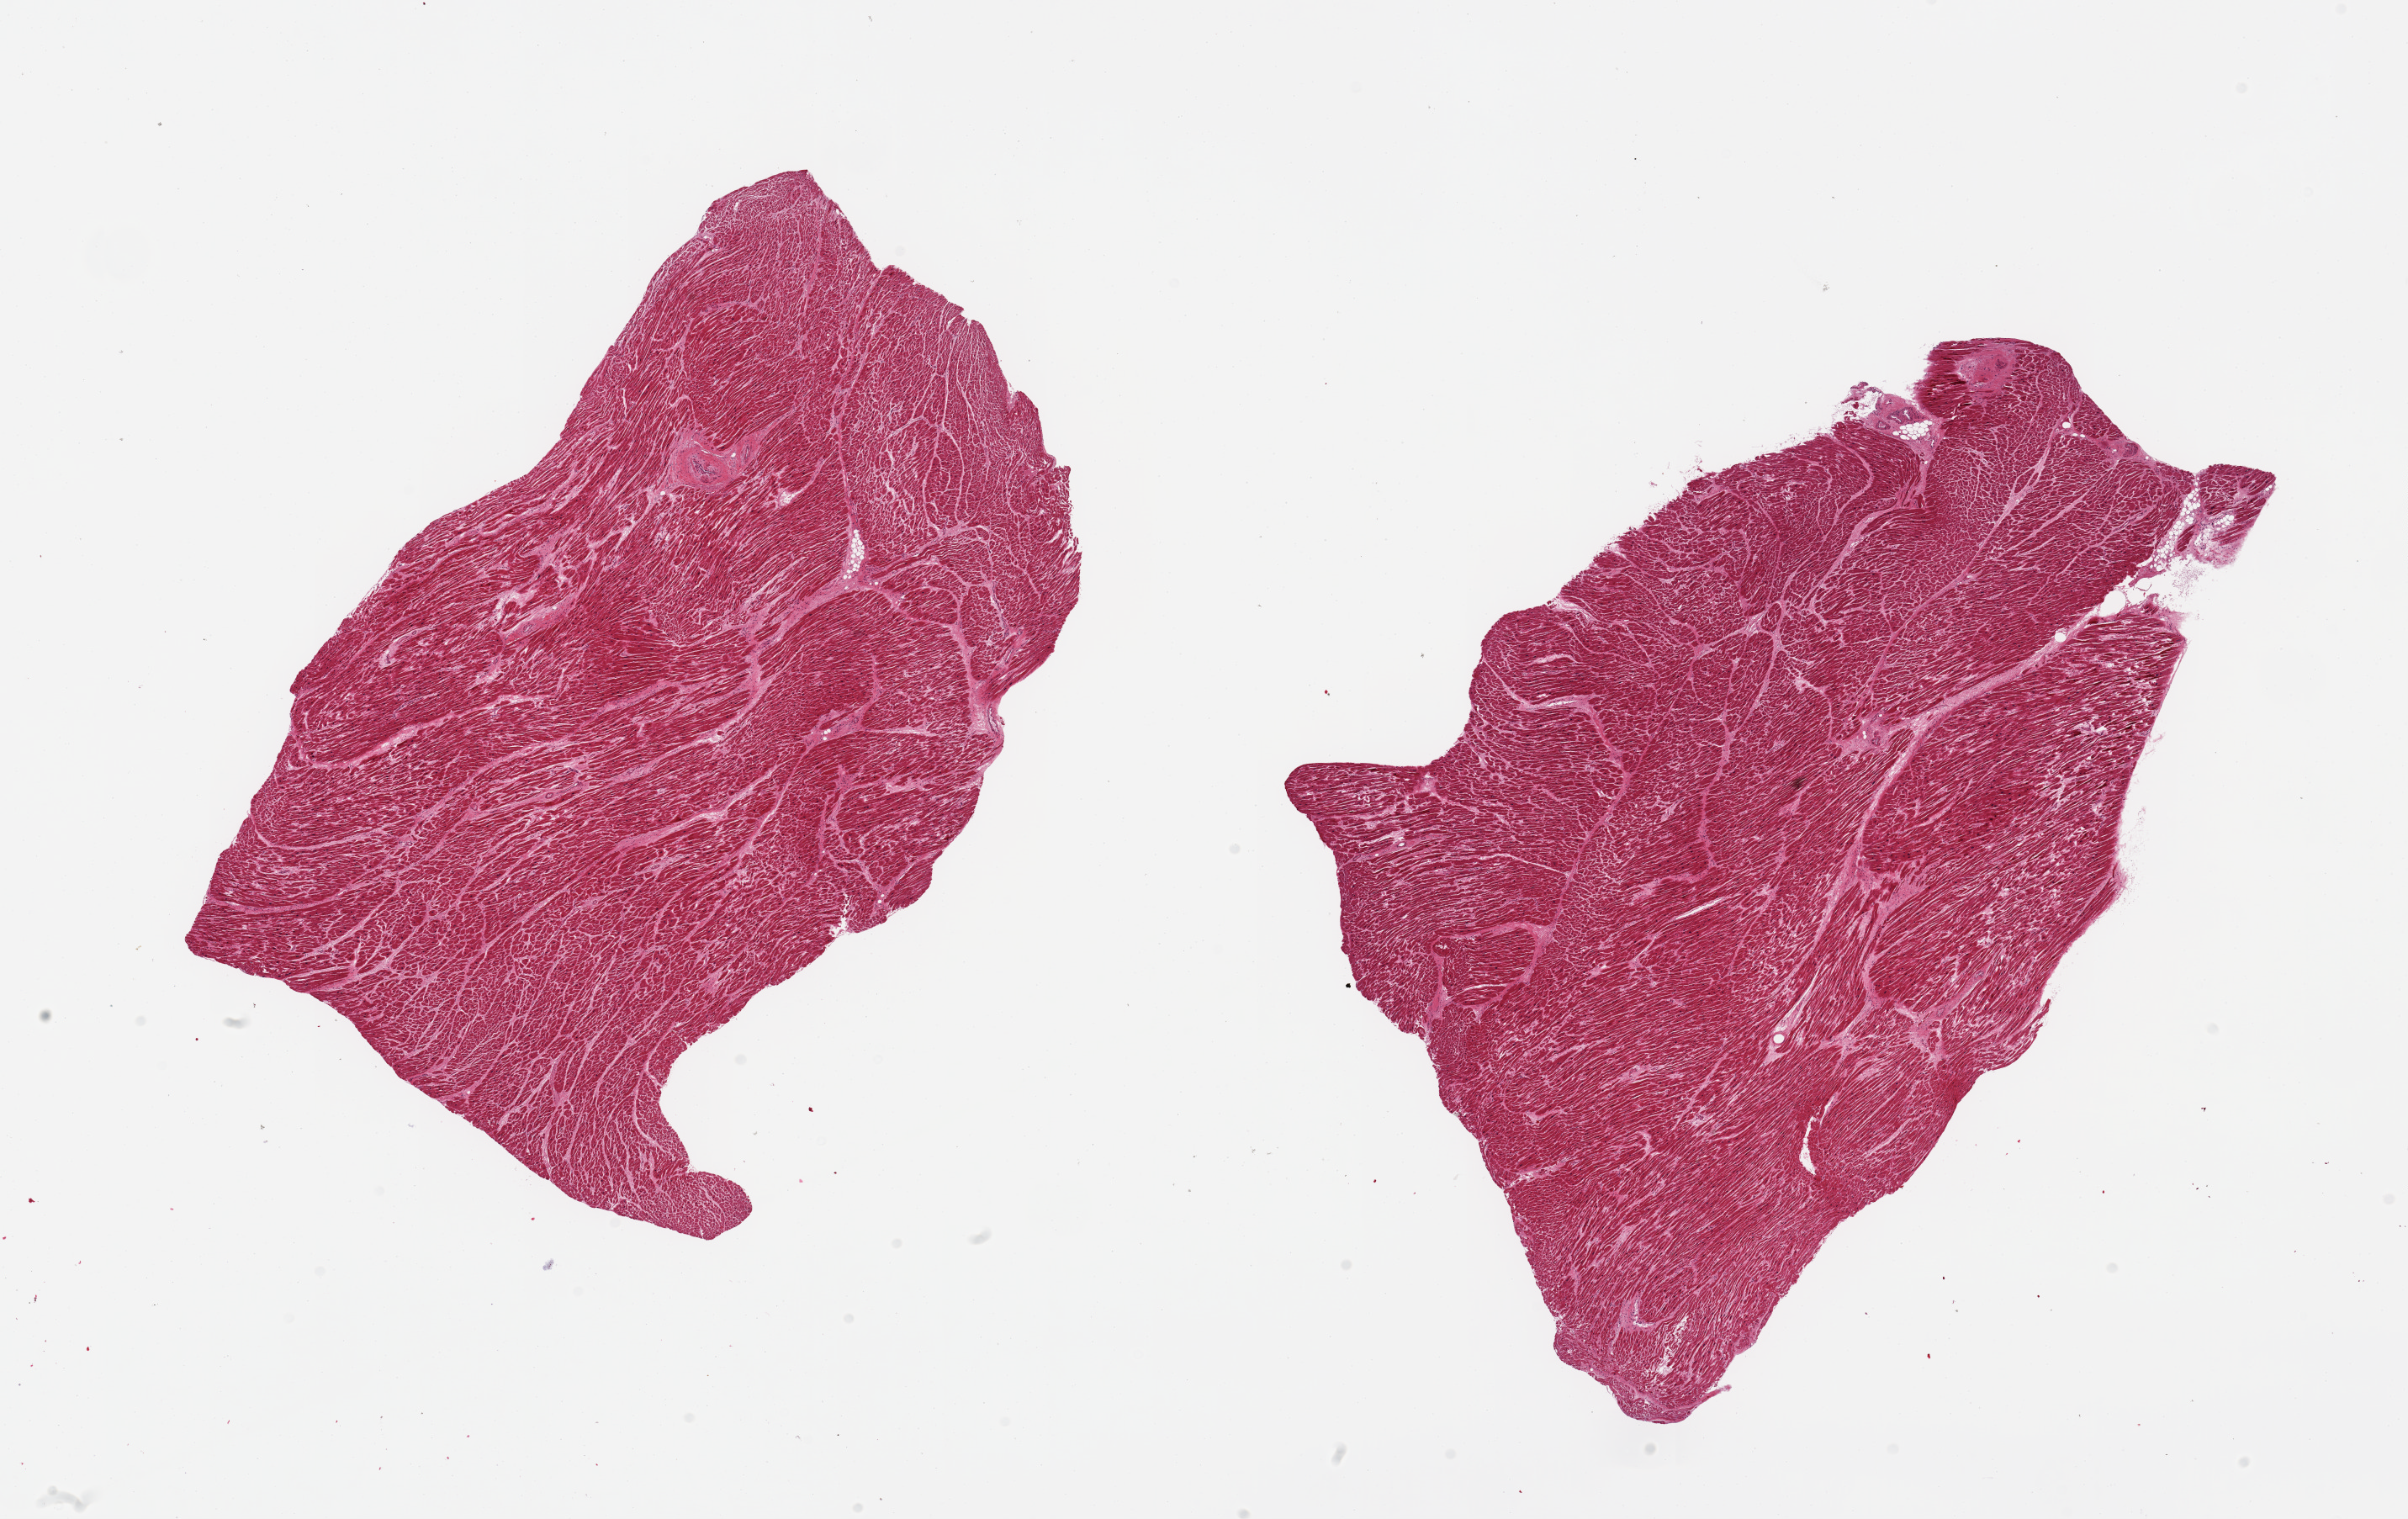
H&E whole-slide image, whole scanned area (about 22.6 x 14.3 mm, from a 20x scan) shown as a low-resolution overview, PAXgene-fixed paraffin-embedded (PFPE) section, section of heart (target tissue), donor tissue sample. Female donor.
* review note (as recorded): 2 pieces